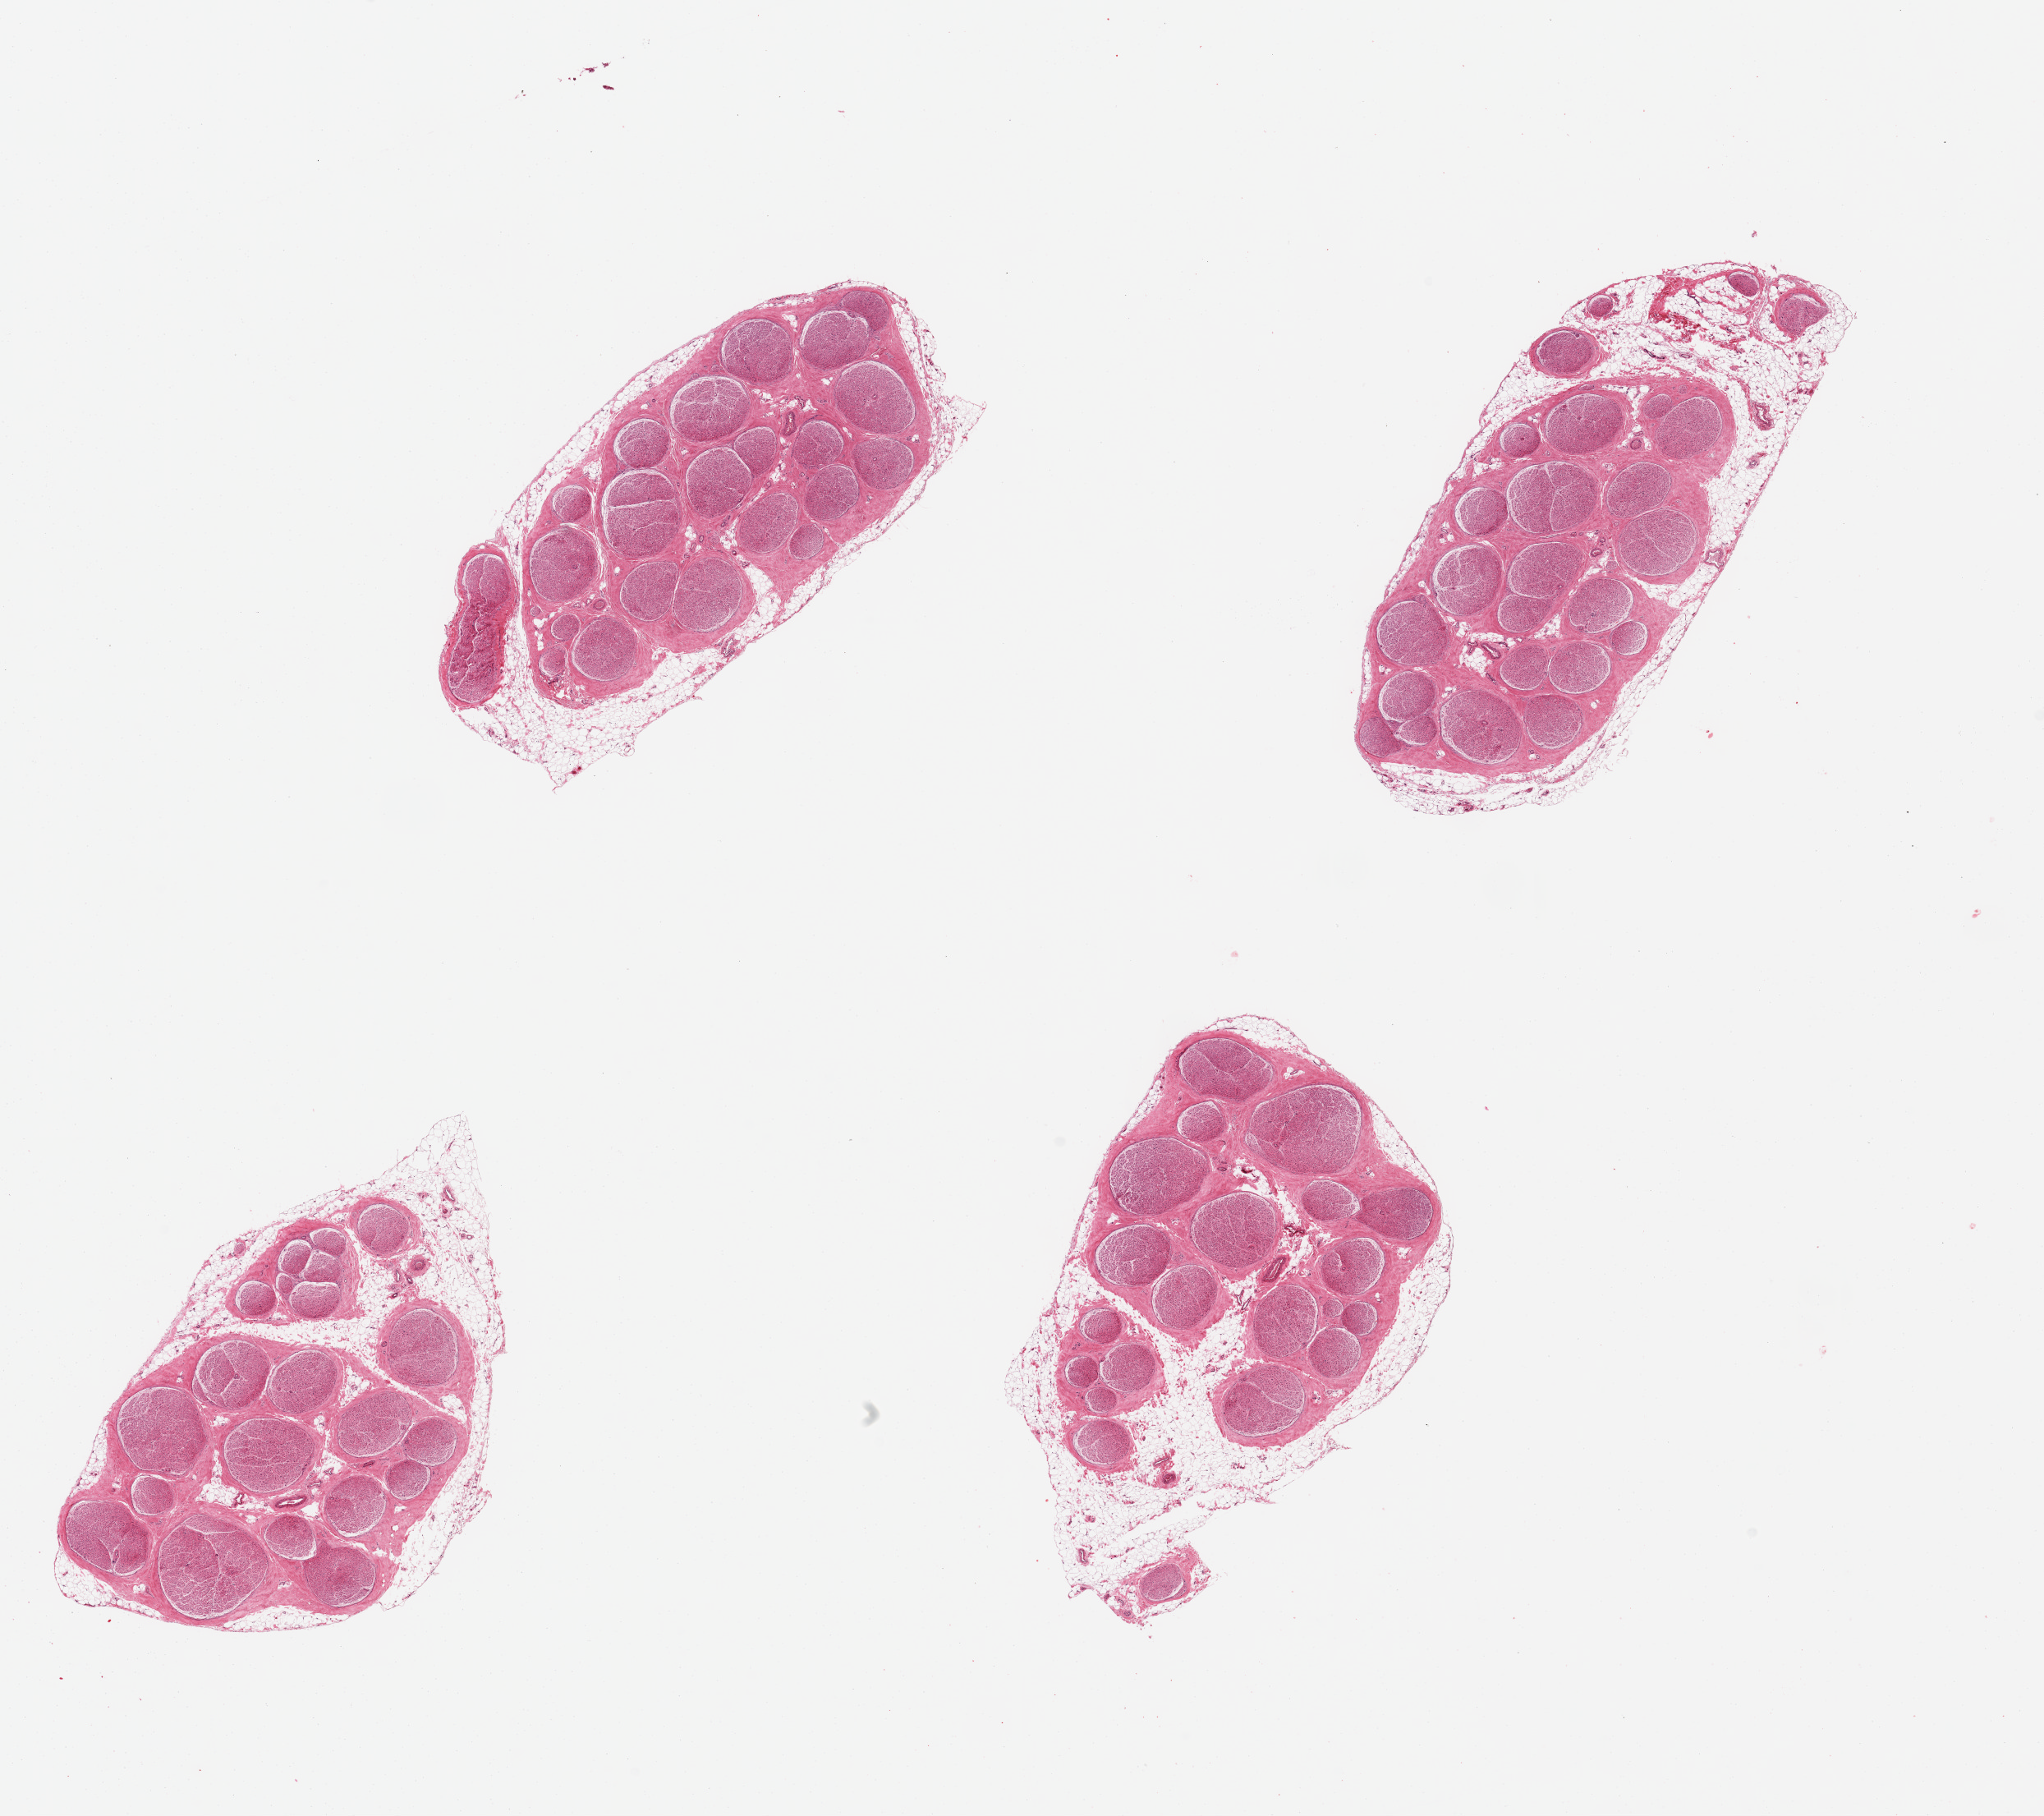
H&E whole-slide image, brightfield — shown as a low-resolution overview of the whole scanned area (about 19.7 x 17.5 mm); PAXgene-fixed, paraffin-embedded tissue; section of tibial nerve (target tissue); donor tissue sample. Donor: male.
Reviewer comment on this tissue sample: 4 pieces, trace adherentnubbins of fat, ~1-2mm.